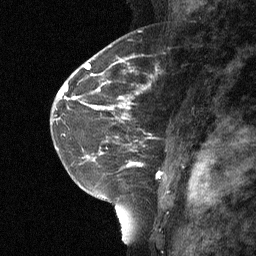
Breast MRI (dynamic contrast-enhanced), one sagittal slice. Position 41 of 64 along the scan axis. Dynamic contrast-enhanced study with each time point stored as its own series, time point 2 of 3 at this slice position (early post-contrast, ordered by acquisition time). 1.5 T. TE 4.8 ms, TR 27 ms. 256 × 256 image matrix. Female patient, age 42 years. Case-level facts recorded for this patient, not image findings: setting: breast cancer imaged before/during neoadjuvant chemotherapy; receptor status: triple-negative.
Outlined on this slice (semi-automatically segmented with operator editing):
- analysis volume of interest (the breast-tissue region the enhancement analysis was run in; not a lesion): bounding box (x1, y1, x2, y2) in pixels: (115, 85, 191, 160)
- tumour enhancement mask (voxels above the 90 % enhancement threshold inside the analysis volume of interest): (120, 86, 146, 119)